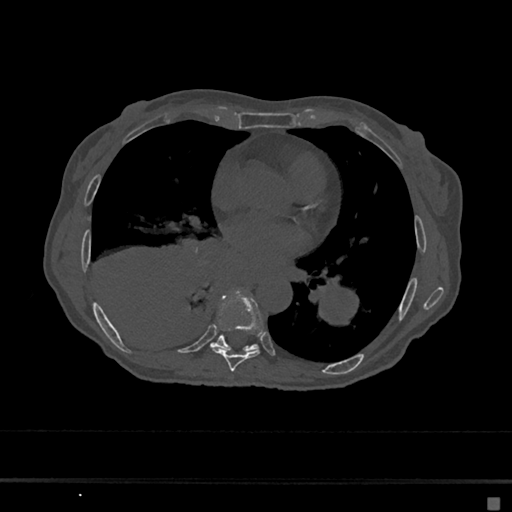
CT including the spine, one axial slice. Slice 353 of 797 in the series (ordered by position). 120 kVp. Bone window (W 1800 / L 400 HU). 0.5 mm slice thickness. 512 × 512 image matrix. Patient: female, 68 years. From the clinical record (not read from this slice): primary cancer: renal.
Structures marked on this image (semi-automatically segmented with operator editing):
- T7 vertebra: bounding box (x1, y1, x2, y2) in pixels: (212, 295, 263, 372)
- T8 vertebra: (211, 335, 258, 352)